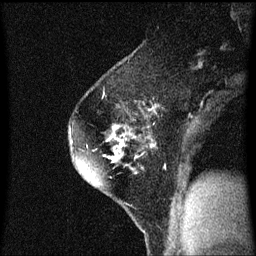
Breast MRI (dynamic contrast-enhanced), one sagittal slice; dynamic contrast-enhanced series, image 2 of 3 at this slice position (ordered by acquisition); 1.5 T; TE 4.2 ms, TR 8.4 ms; 2 mm slice thickness; 256 × 256 image matrix, field of view 200 × 200 mm. Patient: female, 60 years.
Outlined on this slice (semi-automatically segmented with operator editing):
- analysis volume of interest (the breast-tissue region the enhancement analysis was run in; not a lesion): bounding box <68,70,143,195> (left, top, right, bottom; pixels)
- tumour enhancement mask (voxels above the 70 % enhancement threshold inside the analysis volume of interest): <72,126,131,183>